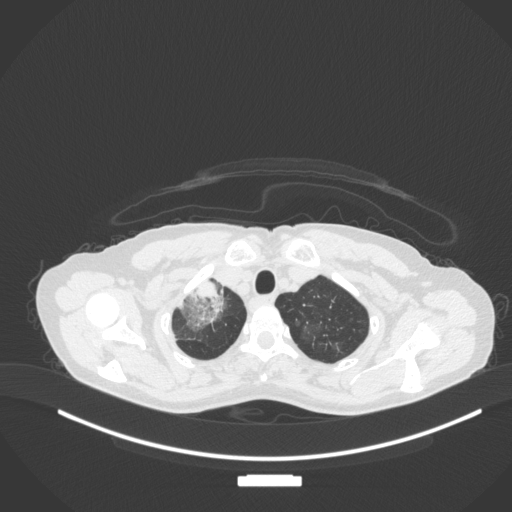
Chest CT, one axial slice. Slice 289 of 311 in the series (ordered by position). 120 kVp. Lung window (W 1500 / L -600 HU). 1 mm slice thickness. 512 × 512 image matrix. Female patient, age 59 years. From the clinical record (not read from this slice): clinical TNM (as recorded): T3 N0 M0; histopathological grade: G1.
Structures marked on this image (bounding box drawn by a radiologist):
- lung tumour (recorded histology: adenocarcinoma): bounding box <177,276,229,333> (left, top, right, bottom; pixels)